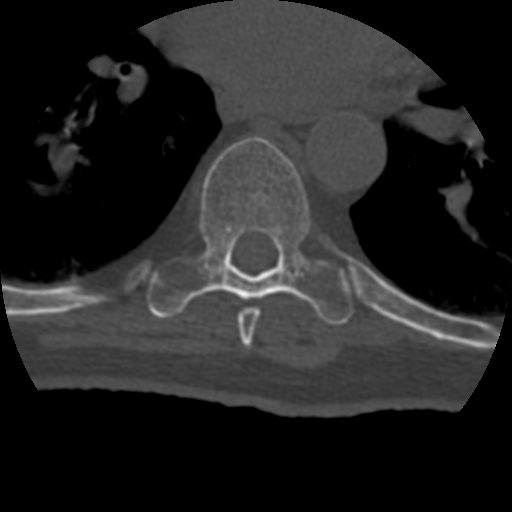
CT including the spine, one axial slice. Position 264 of 399 along the scan axis. 120 kVp. Bone window (W 1800 / L 400 HU). 1.25 mm slice thickness. 512 × 512 image matrix. Patient age 69 years. From the clinical record (not read from this slice): primary cancer: prostate.
Outlined on this slice (semi-automatically segmented with operator editing):
- T7 vertebra: bounding box <238,307,261,348> (left, top, right, bottom; pixels)
- T8 vertebra: <146,136,354,325>